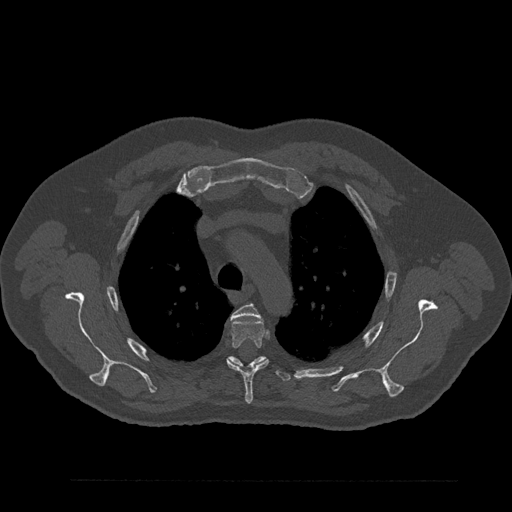
CT including the spine, one axial slice. Reconstruction kernel Br40s/3. Bone window (W 1800 / L 400 HU). 0.5 mm slice thickness. 512 × 512 image matrix, field of view 430 × 430 mm. Male patient, age 61 years. Case-level facts recorded for this patient, not image findings: primary cancer: prostate.
Outlined on this slice (semi-automatic segmentation, software-assisted and operator-edited):
- T3 vertebra: box from (x=231, y=304) to (x=260, y=319) px
- T4 vertebra: (x=227, y=319)–(x=269, y=404)
- T5 vertebra: (x=229, y=356)–(x=291, y=381)